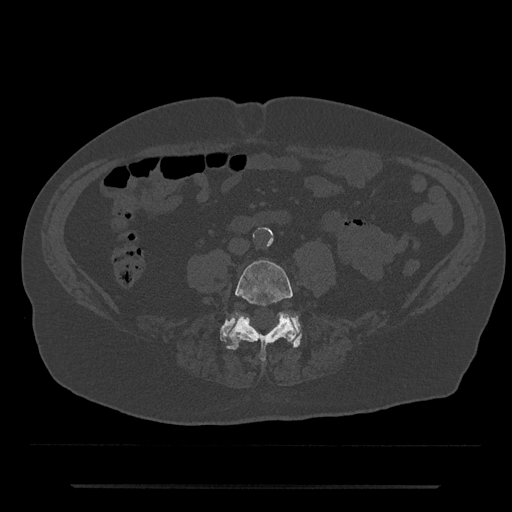
CT including the spine, one axial slice. Position 338 of 797 along the scan axis. 120 kVp. Bone window (W 1800 / L 400 HU). 0.5 mm slice thickness. 512 × 512 image matrix. Patient: male, 80 years. Case-level facts recorded for this patient, not image findings: primary cancer: prostate; vertebrae with lytic lesions (as recorded): L1, T11.
Outlined on this slice (semi-automatic segmentation, software-assisted and operator-edited):
- L4 vertebra: bounding box [x1, y1, x2, y2] px = [228, 260, 297, 361]
- L5 vertebra: [219, 314, 302, 347]